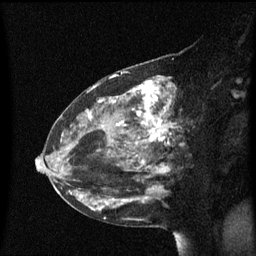
Breast MRI (dynamic contrast-enhanced), one sagittal slice. Slice 33 of 60 in the series (ordered by position). Dynamic contrast-enhanced series, image 2 of 3 at this slice position (ordered by acquisition). 1.5 T. TE 4.2 ms, TR 8.4 ms. 2 mm slice thickness. 256 × 256 image matrix, field of view 200 × 200 mm. Patient: female, 48 years. From the clinical record (not read from this slice): setting: breast cancer imaged before/during neoadjuvant chemotherapy; receptor status: HR-positive, HER2-negative.
Structures marked on this image (semi-automatic segmentation, software-assisted and operator-edited):
- analysis volume of interest (the breast-tissue region the enhancement analysis was run in; not a lesion): bounding box <80,78,189,220> (left, top, right, bottom; pixels)
- tumour enhancement mask (voxels above the 70 % enhancement threshold inside the analysis volume of interest): <86,81,175,211>